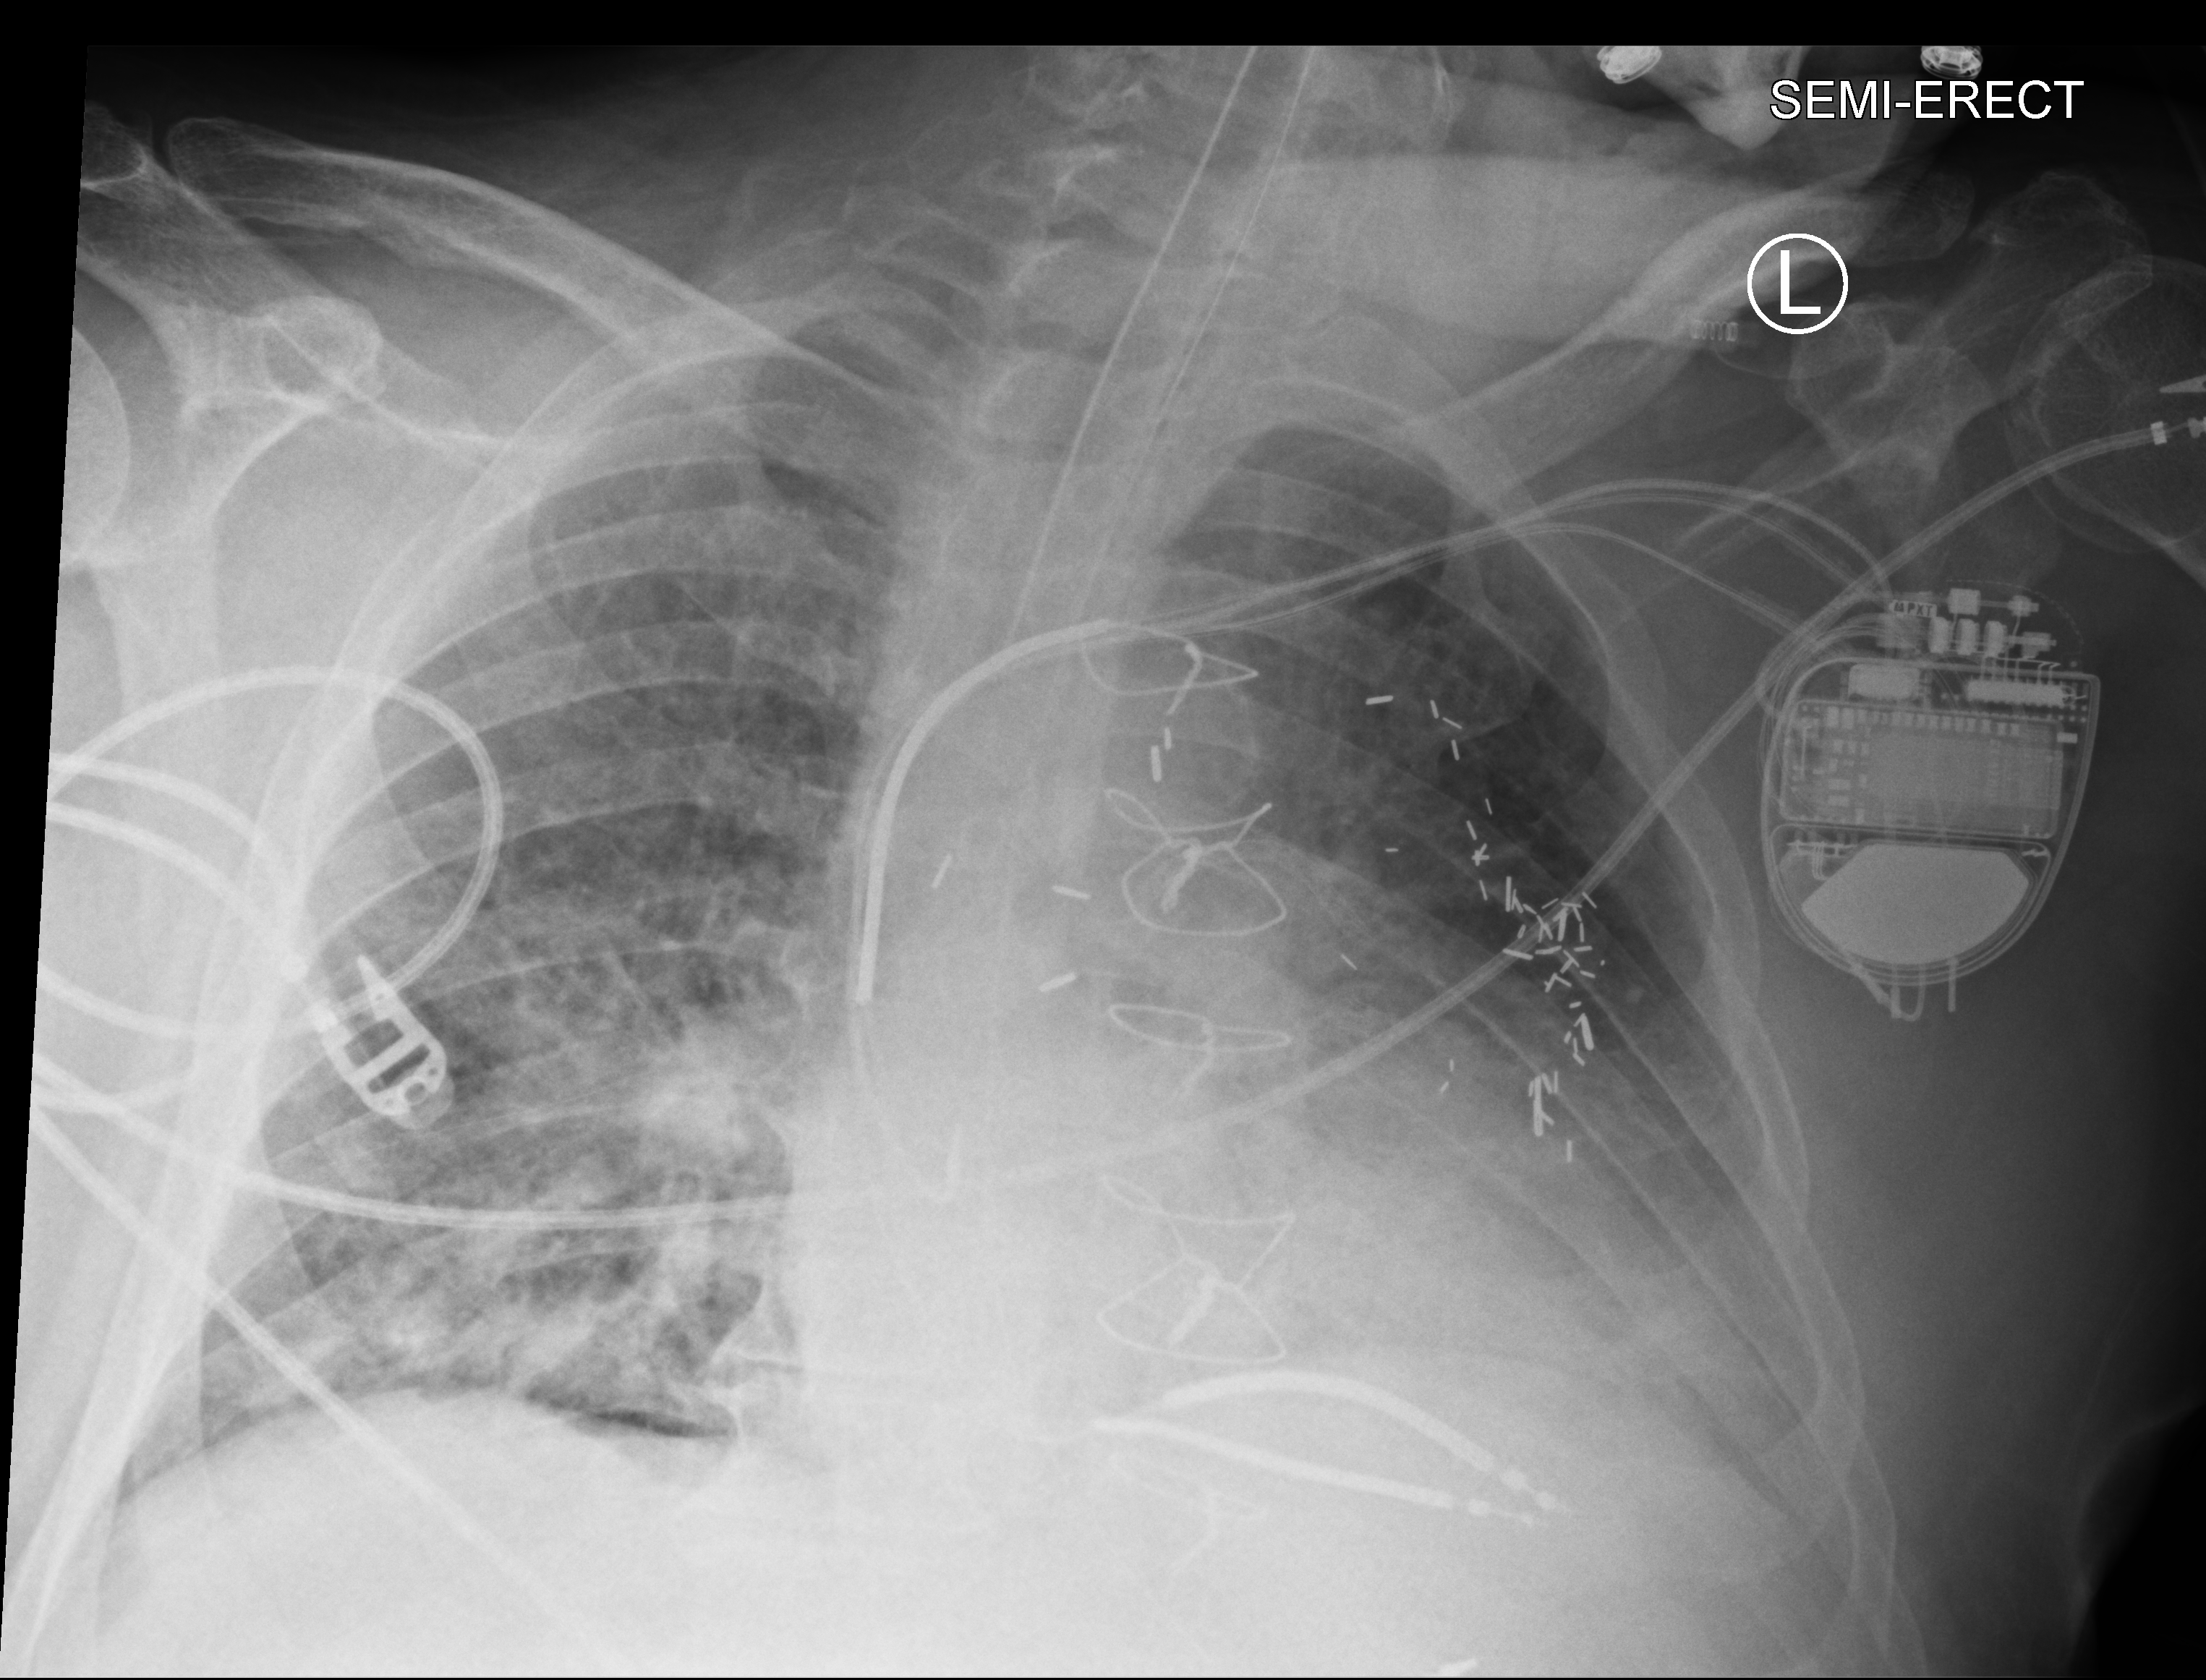
Portable chest radiograph. Patient hospitalised with COVID-19; male, aged 60–74 years.
Hospital-stay facts (about this admission, not read from this image; timing relative to this image not recorded): smoking status (admission record): never; COPD (admission record): no.